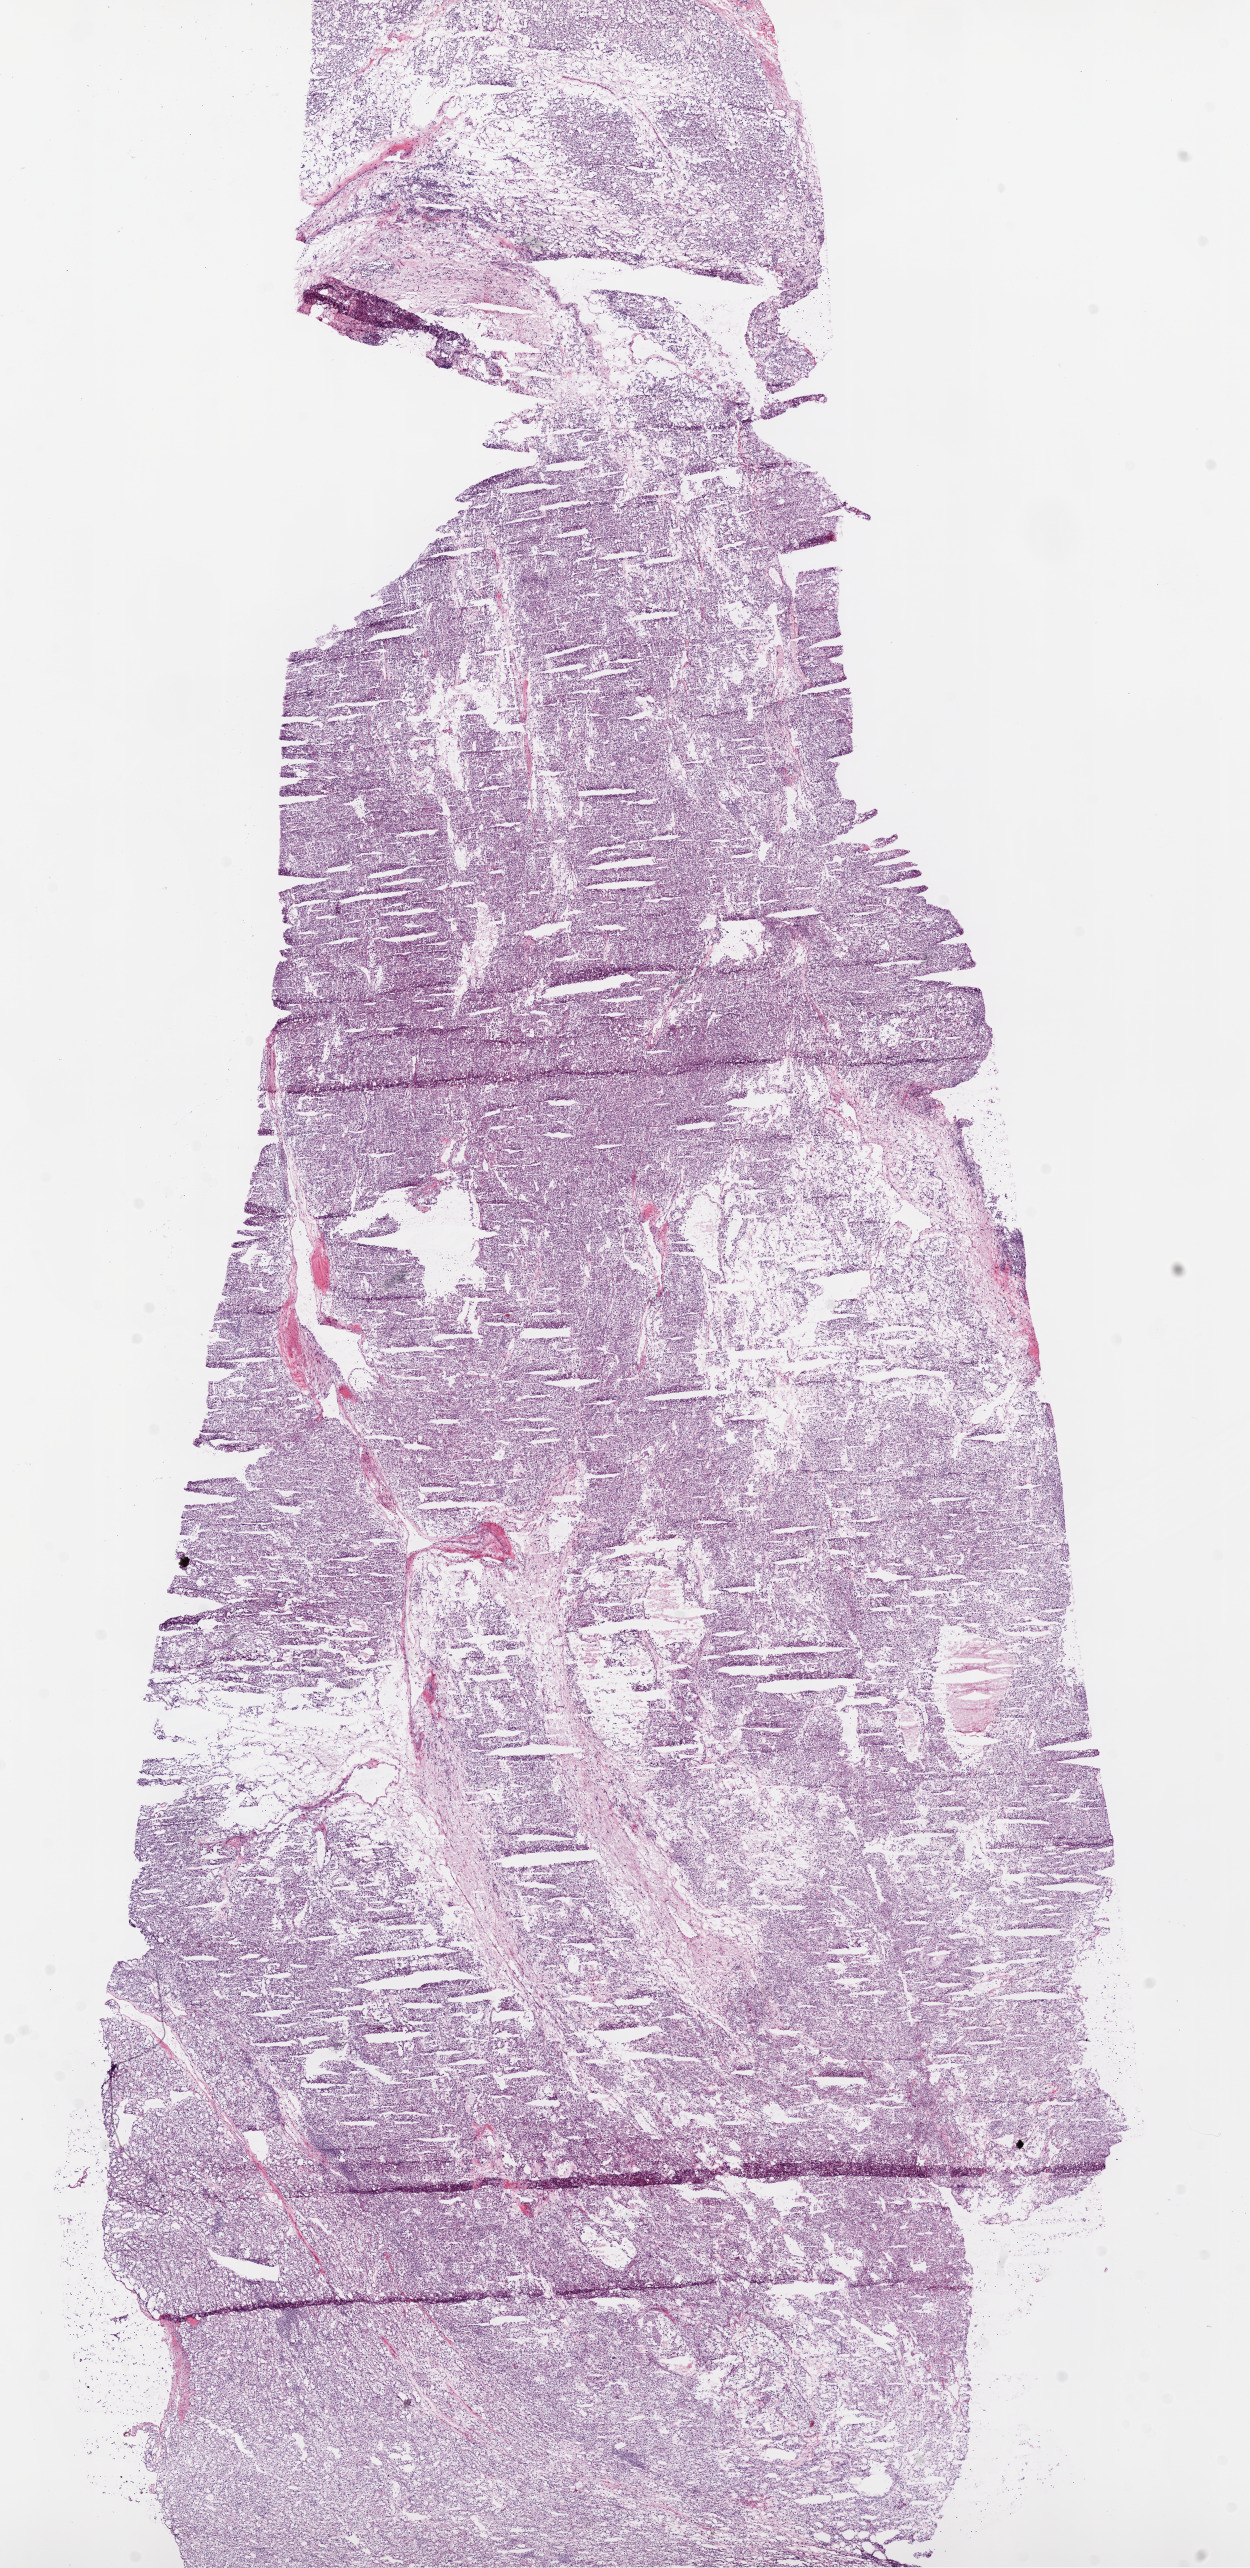
H&E-stained whole-slide image — whole scanned area (about 10.0 x 20.6 mm, acquisition: 20x scan) shown as a low-resolution overview. Frozen section from the bottom of the tissue portion. Primary tumour sample from the kidney. Patient: male, age at initial diagnosis 73 years.
Pathologic diagnosis: Clear cell adenocarcinoma, NOS.